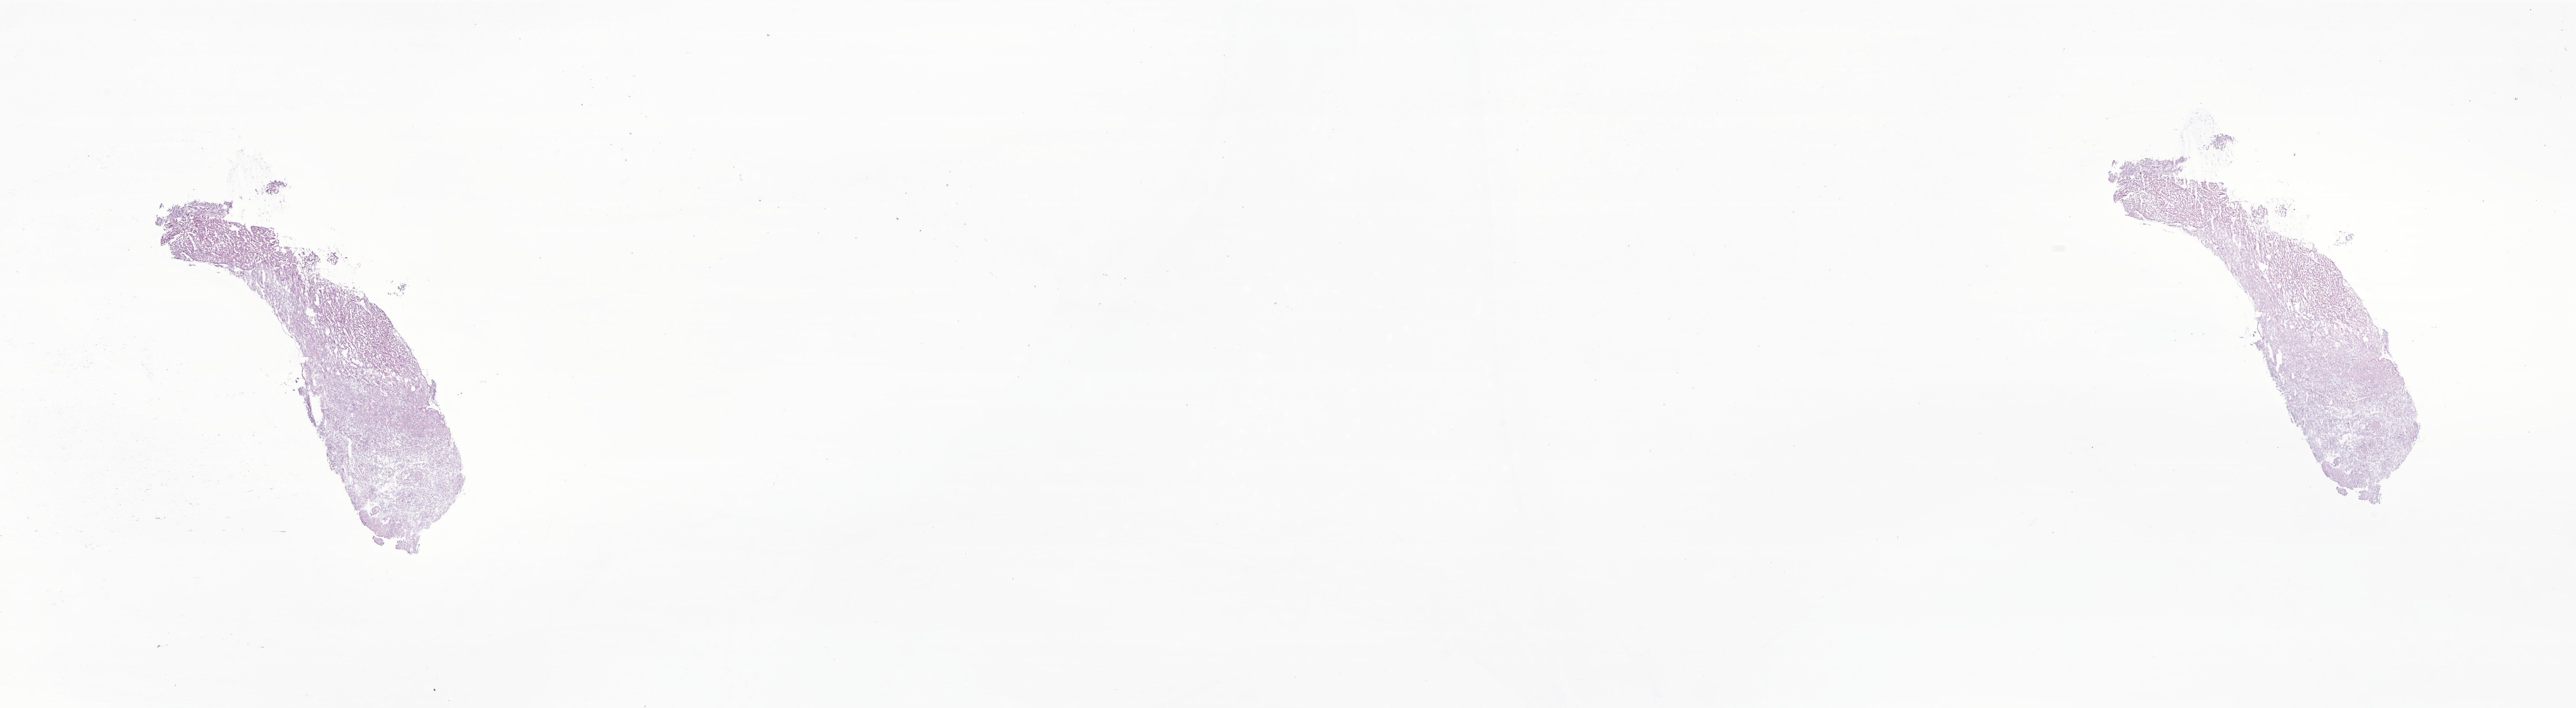
Digitized hematoxylin and eosin (H&E)-stained section of tumor tissue from the brain, whole scanned area (about 32.0 x 8.8 mm) shown as a low-resolution overview. Frozen section (OCT-embedded). Patient: male, age 726 days (about 2.0 years).
- diagnosis: Pilocytic astrocytoma